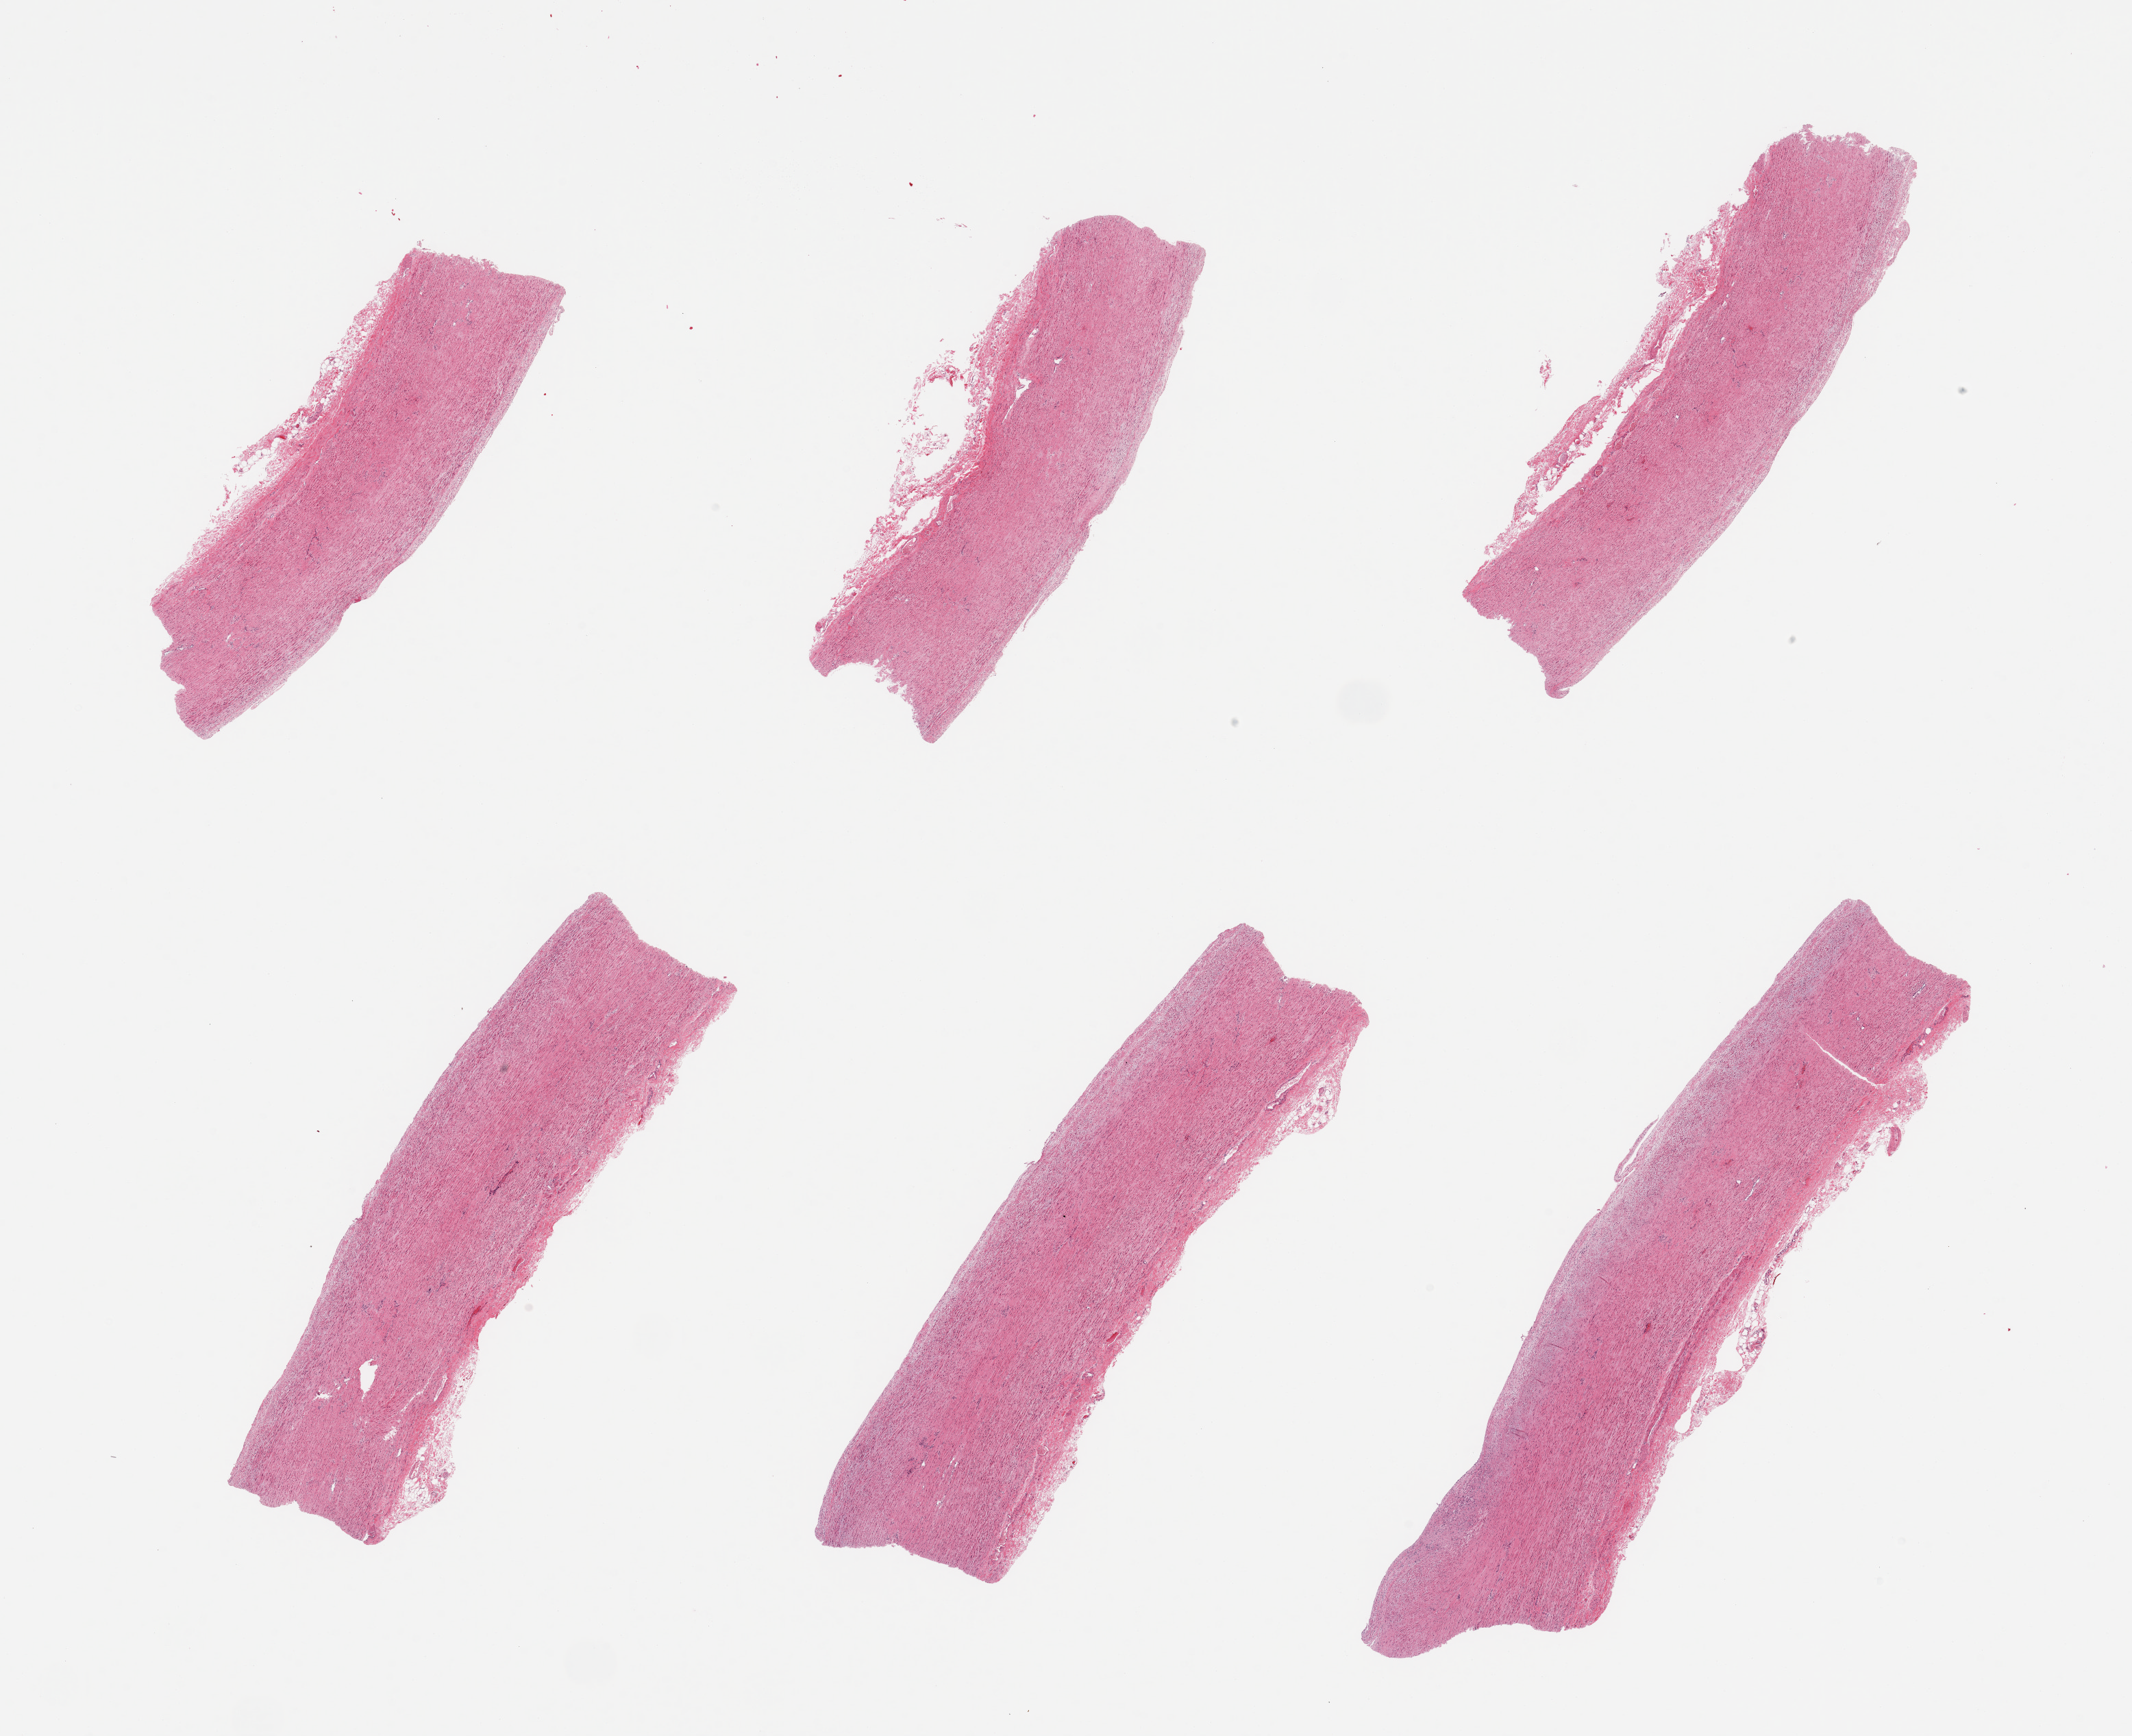
Whole-slide image, hematoxylin and eosin (H&E) stain, brightfield — shown as a low-resolution overview of the whole scanned area (about 24.6 x 20.0 mm, slide scanned at 20x), PAXgene-fixed paraffin-embedded (PFPE) section, target tissue: aorta, tissue donor sample. Male donor.
- pathologist's review note for this sample: 6 pieces; mild flat plaques